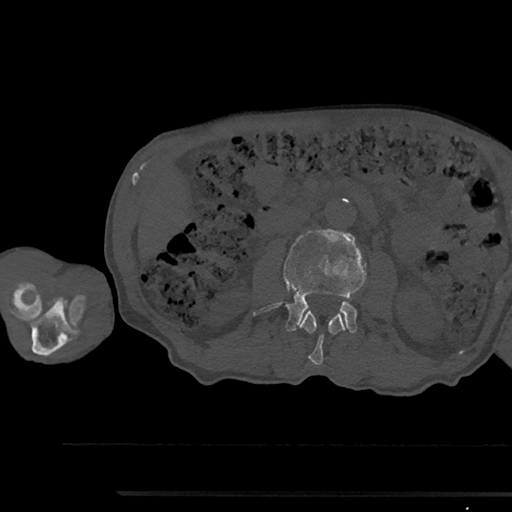
CT including the spine, one axial slice. Position 521 of 797 along the scan axis. Reconstruction kernel Br40s/3. Bone window (W 1800 / L 400 HU). 0.5 mm slice thickness. 512 × 512 image matrix, field of view 367 × 367 mm. Male patient, age 79 years. From the clinical record (not read from this slice): primary cancer: prostate.
Structures marked on this image (semi-automatic segmentation, software-assisted and operator-edited):
- L2 vertebra: bounding box [x1, y1, x2, y2] px = [299, 310, 346, 365]
- L3 vertebra: [253, 230, 367, 333]